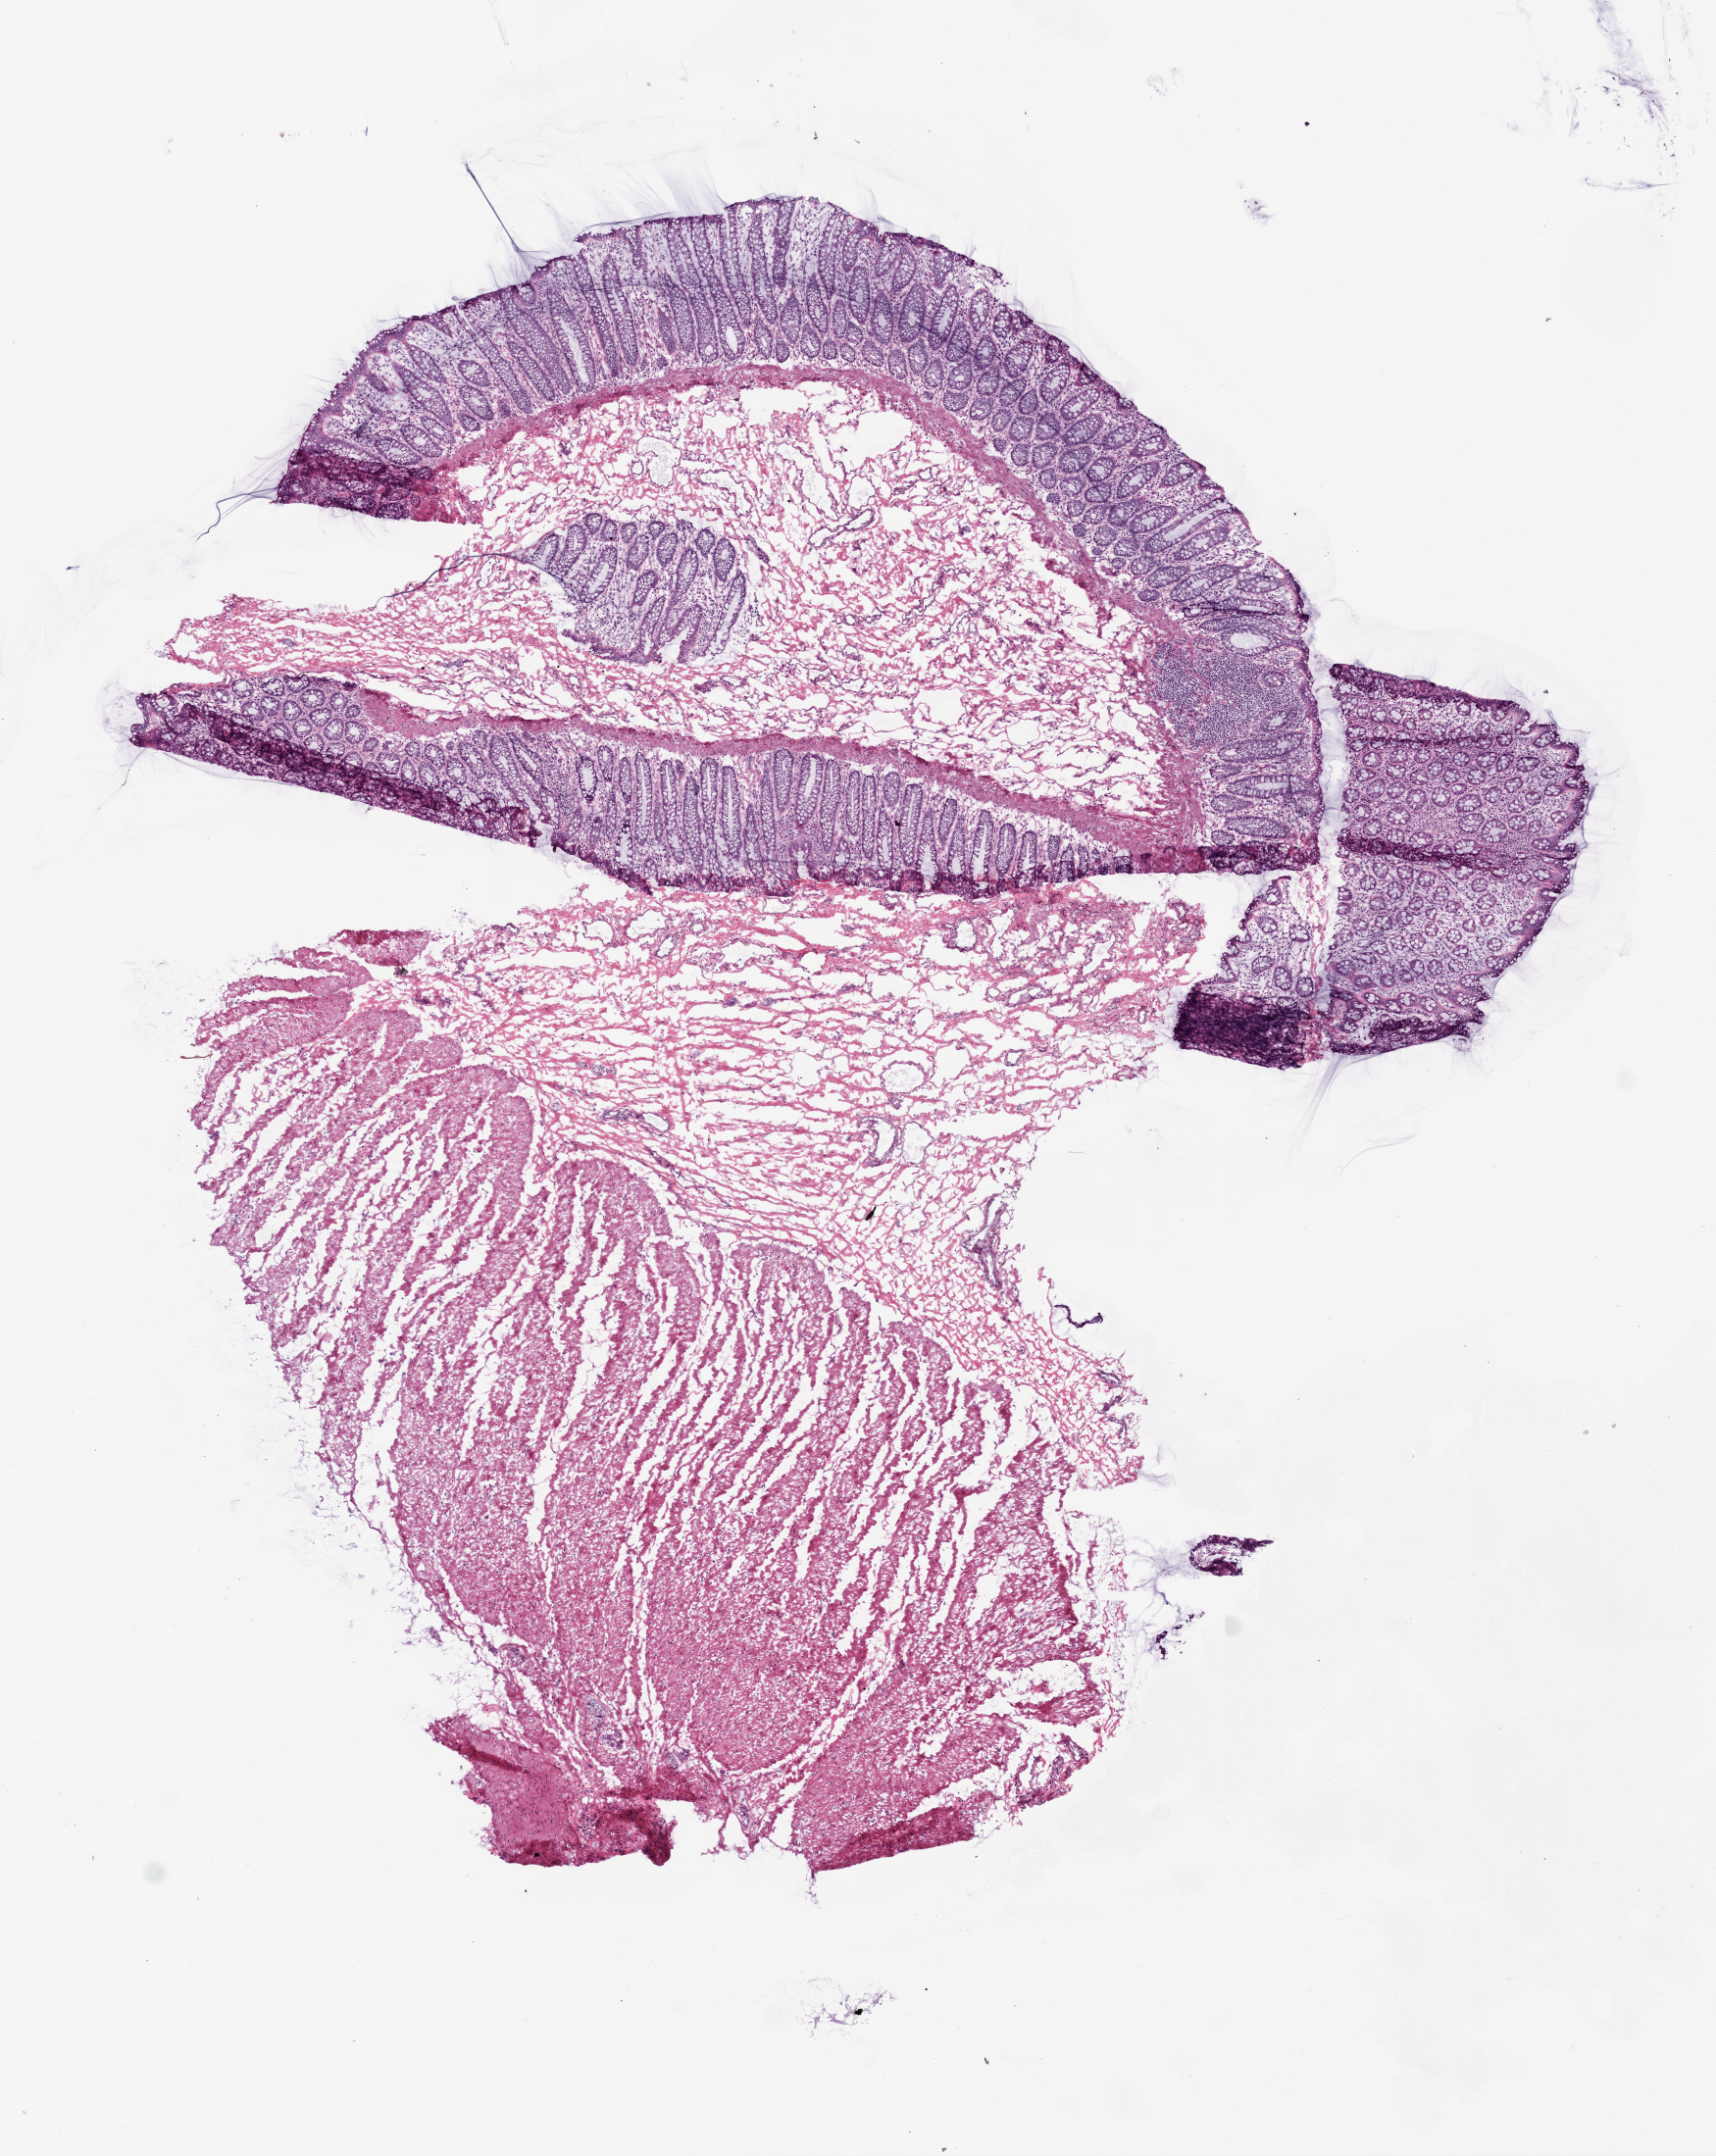
H&E-stained whole-slide image — whole scanned area (about 7.0 x 8.8 mm) shown as a low-resolution overview, frozen section from the top of the tissue portion, rectum, solid tissue normal (non-tumour tissue) sample. Female patient.
This section: solid tissue normal sample (biorepository sample class). Patient diagnosis: Adenocarcinoma, NOS (rectosigmoid junction).